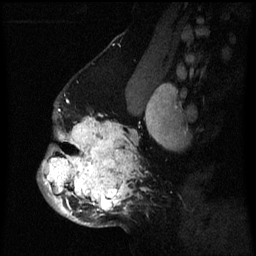
Breast MRI (dynamic contrast-enhanced), one sagittal slice; slice 41 of 60 in the series (ordered by position); dynamic contrast-enhanced series, image 2 of 3 at this slice position (ordered by acquisition); 1.5 T; TE 4.2 ms, TR 8 ms; 2 mm slice thickness; 256 × 256 image matrix, field of view 190 × 190 mm. Patient: female, 50 years.
Structures marked on this image (semi-automatic segmentation, software-assisted and operator-edited):
- analysis volume of interest (the breast-tissue region the enhancement analysis was run in; not a lesion): bounding box <37,114,138,227> (left, top, right, bottom; pixels)
- tumour enhancement mask (voxels above the 70 % enhancement threshold inside the analysis volume of interest): <42,115,137,225>